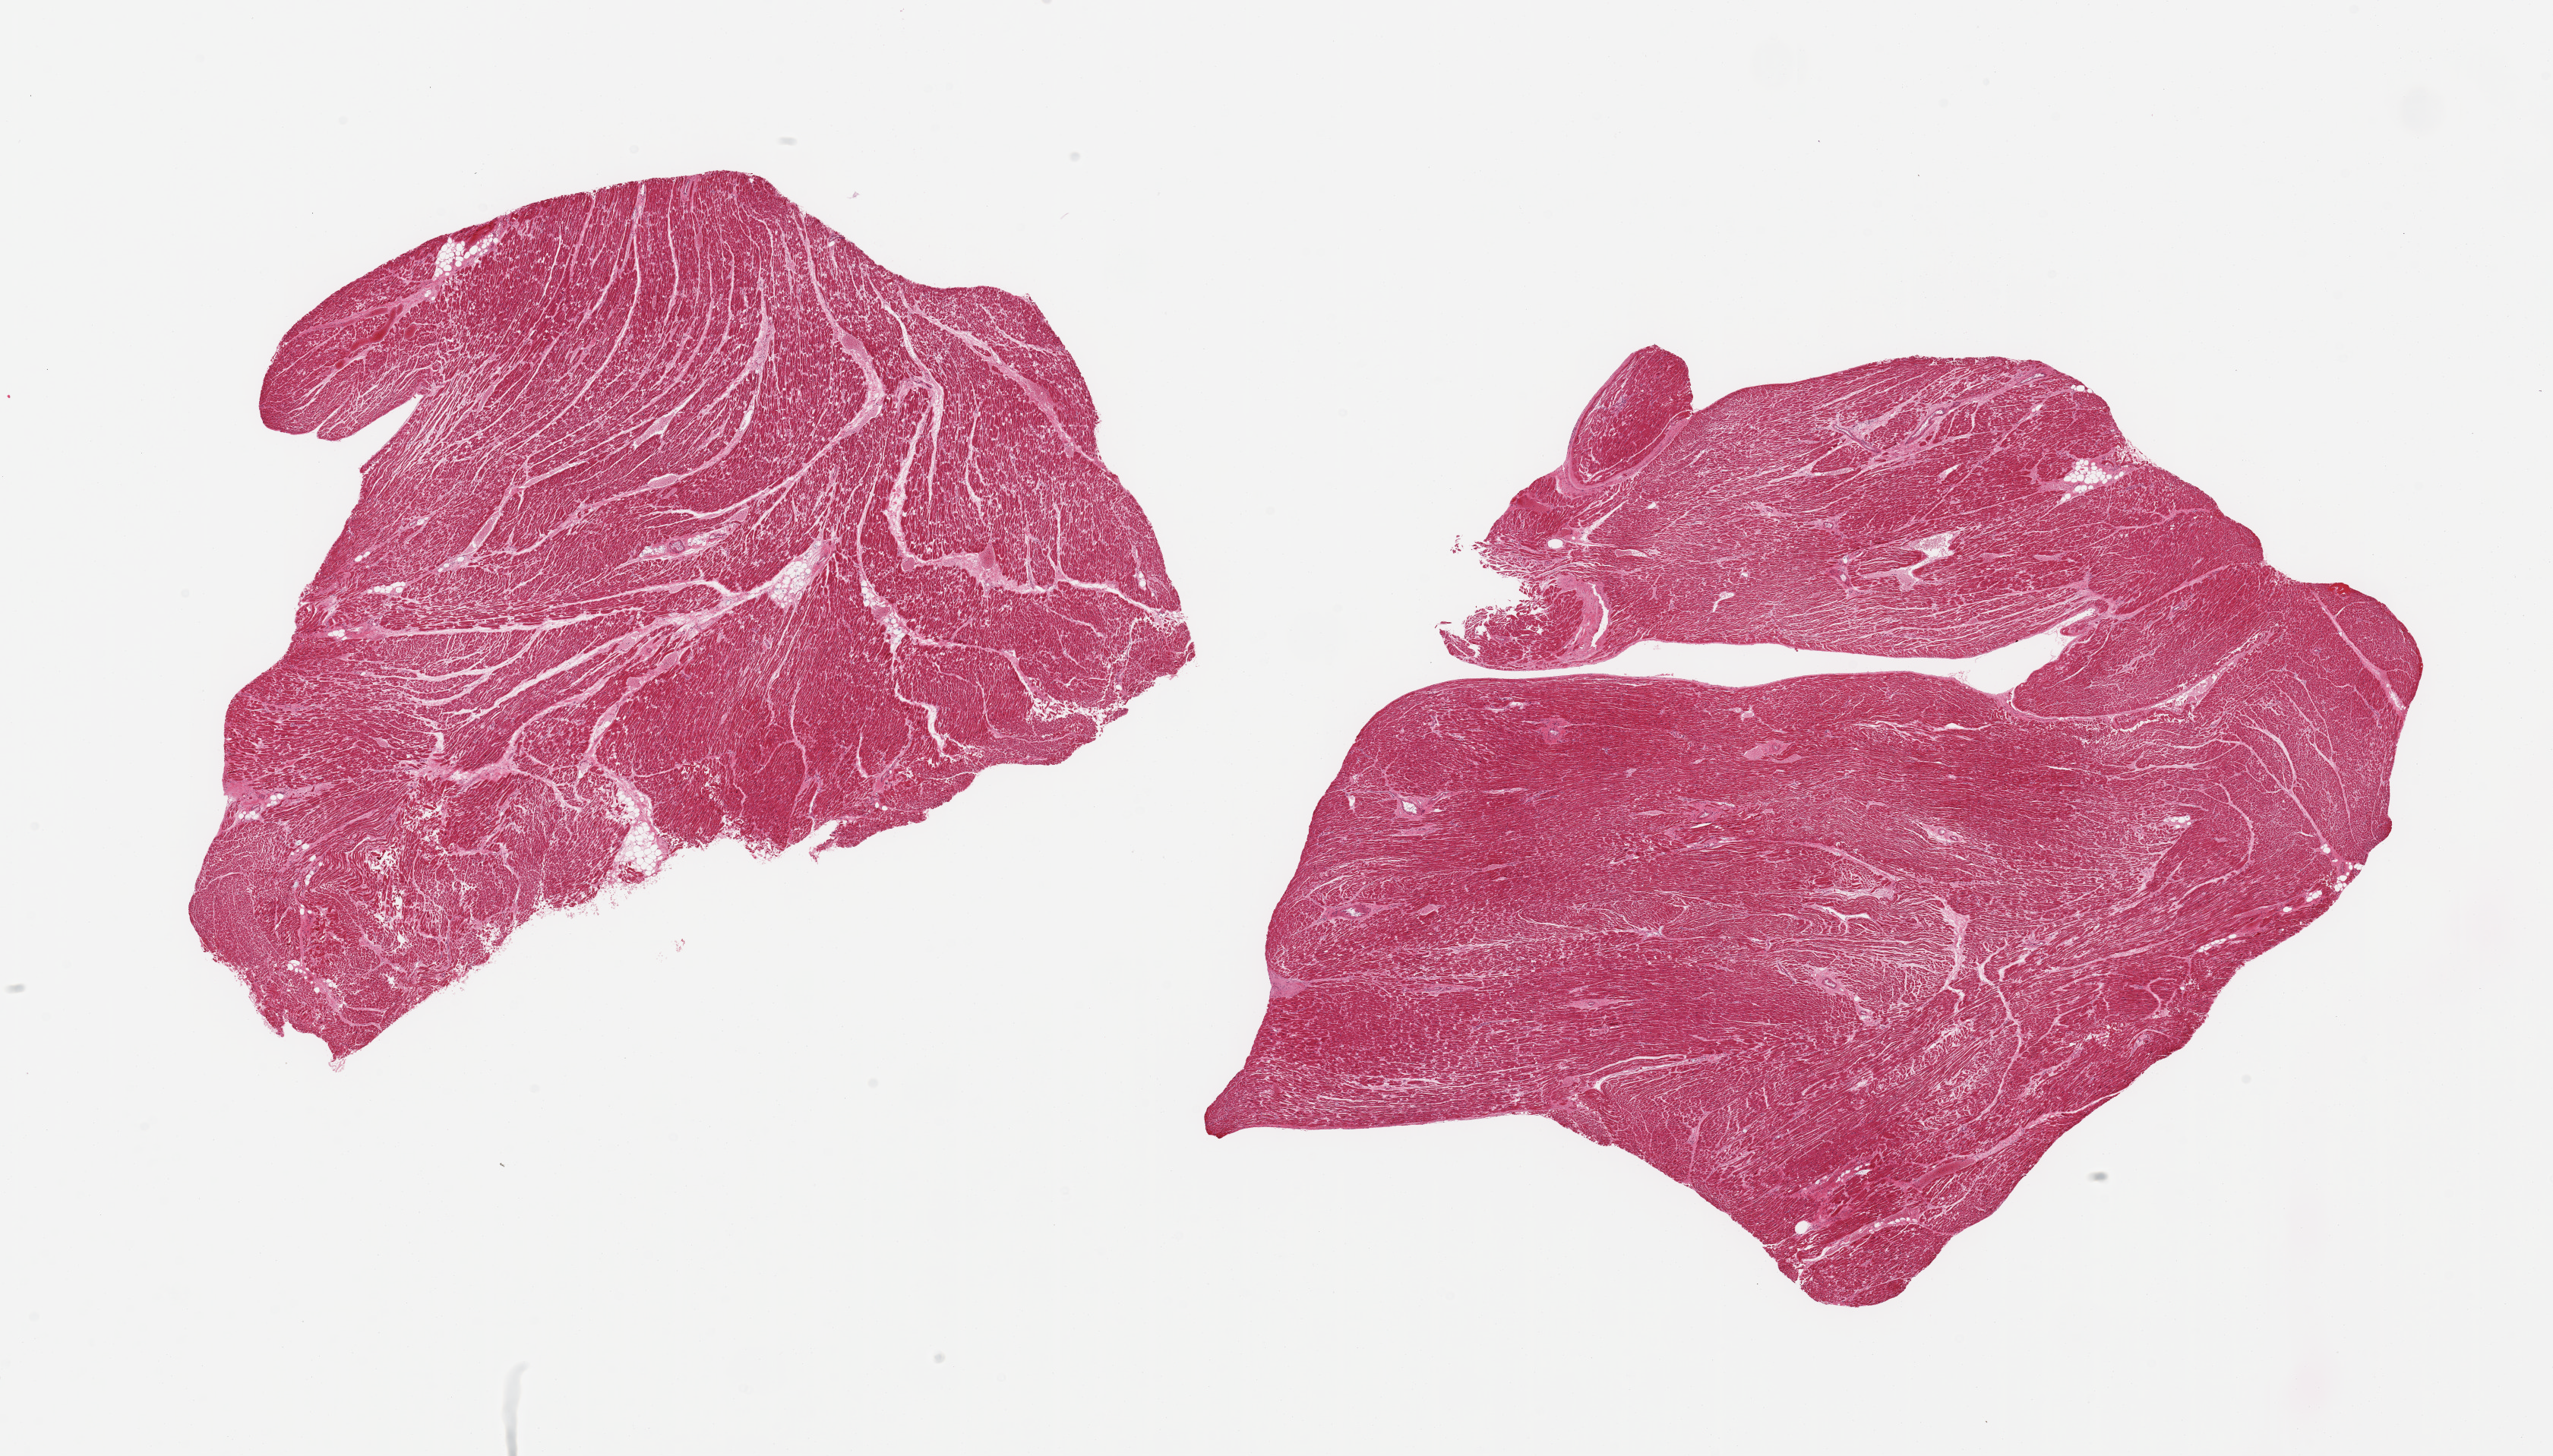
Digitized haematoxylin and eosin-stained section, a low-resolution overview of the entire scanned area, about 26.6 x 15.2 mm (from a 20x scan); PAXgene-fixed, paraffin-embedded tissue; target tissue: heart; tissue donor sample. Donor sex: male.
- pathologist's review note for this sample: 2 pieces; numerous artefactual 'cracked' myofibers; no active or chronic lesions